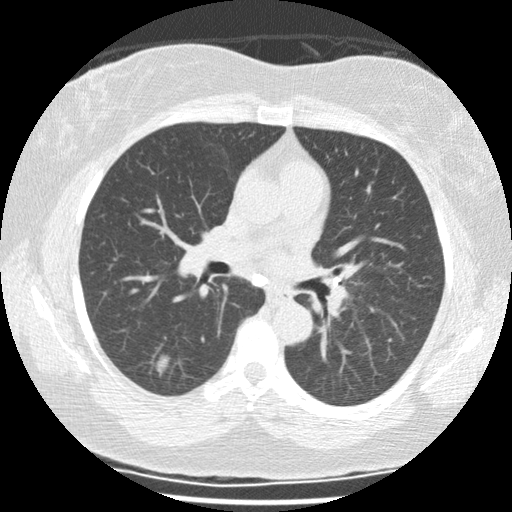
Low-dose screening chest CT, one axial slice. Slice 65 of 117 in the series (ordered by position). 120 kVp. Lung window (W 1500 / L -600 HU). 512 × 512 image matrix, field of view 325 × 325 mm.
Outlined on this slice (manually delineated by an expert):
- lesion 1 (tumor, lower lobe of right lung): bounding box (x1, y1, x2, y2) in pixels: (156, 355, 170, 375)